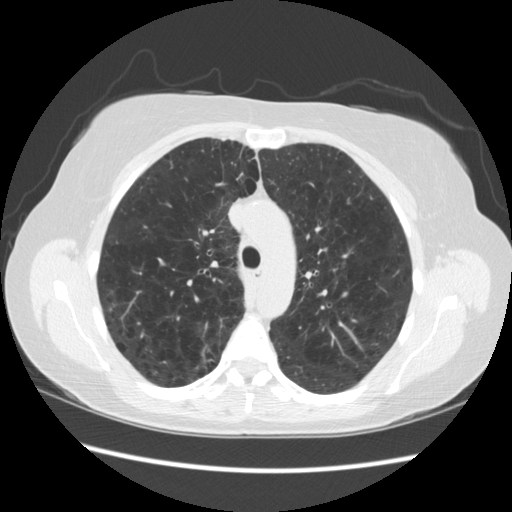
Low-dose screening chest CT, one axial slice. Slice 167 of 235 in the series (ordered by position). Lung window (W 1500 / L -600 HU). 2.5 mm slice thickness. 512 × 512 image matrix, field of view 360 × 360 mm.
Outlined on this slice (outlined manually by an expert reader):
- lesion 1 (tumor, upper lobe of right lung): bounding box <200,343,216,364> (left, top, right, bottom; pixels)